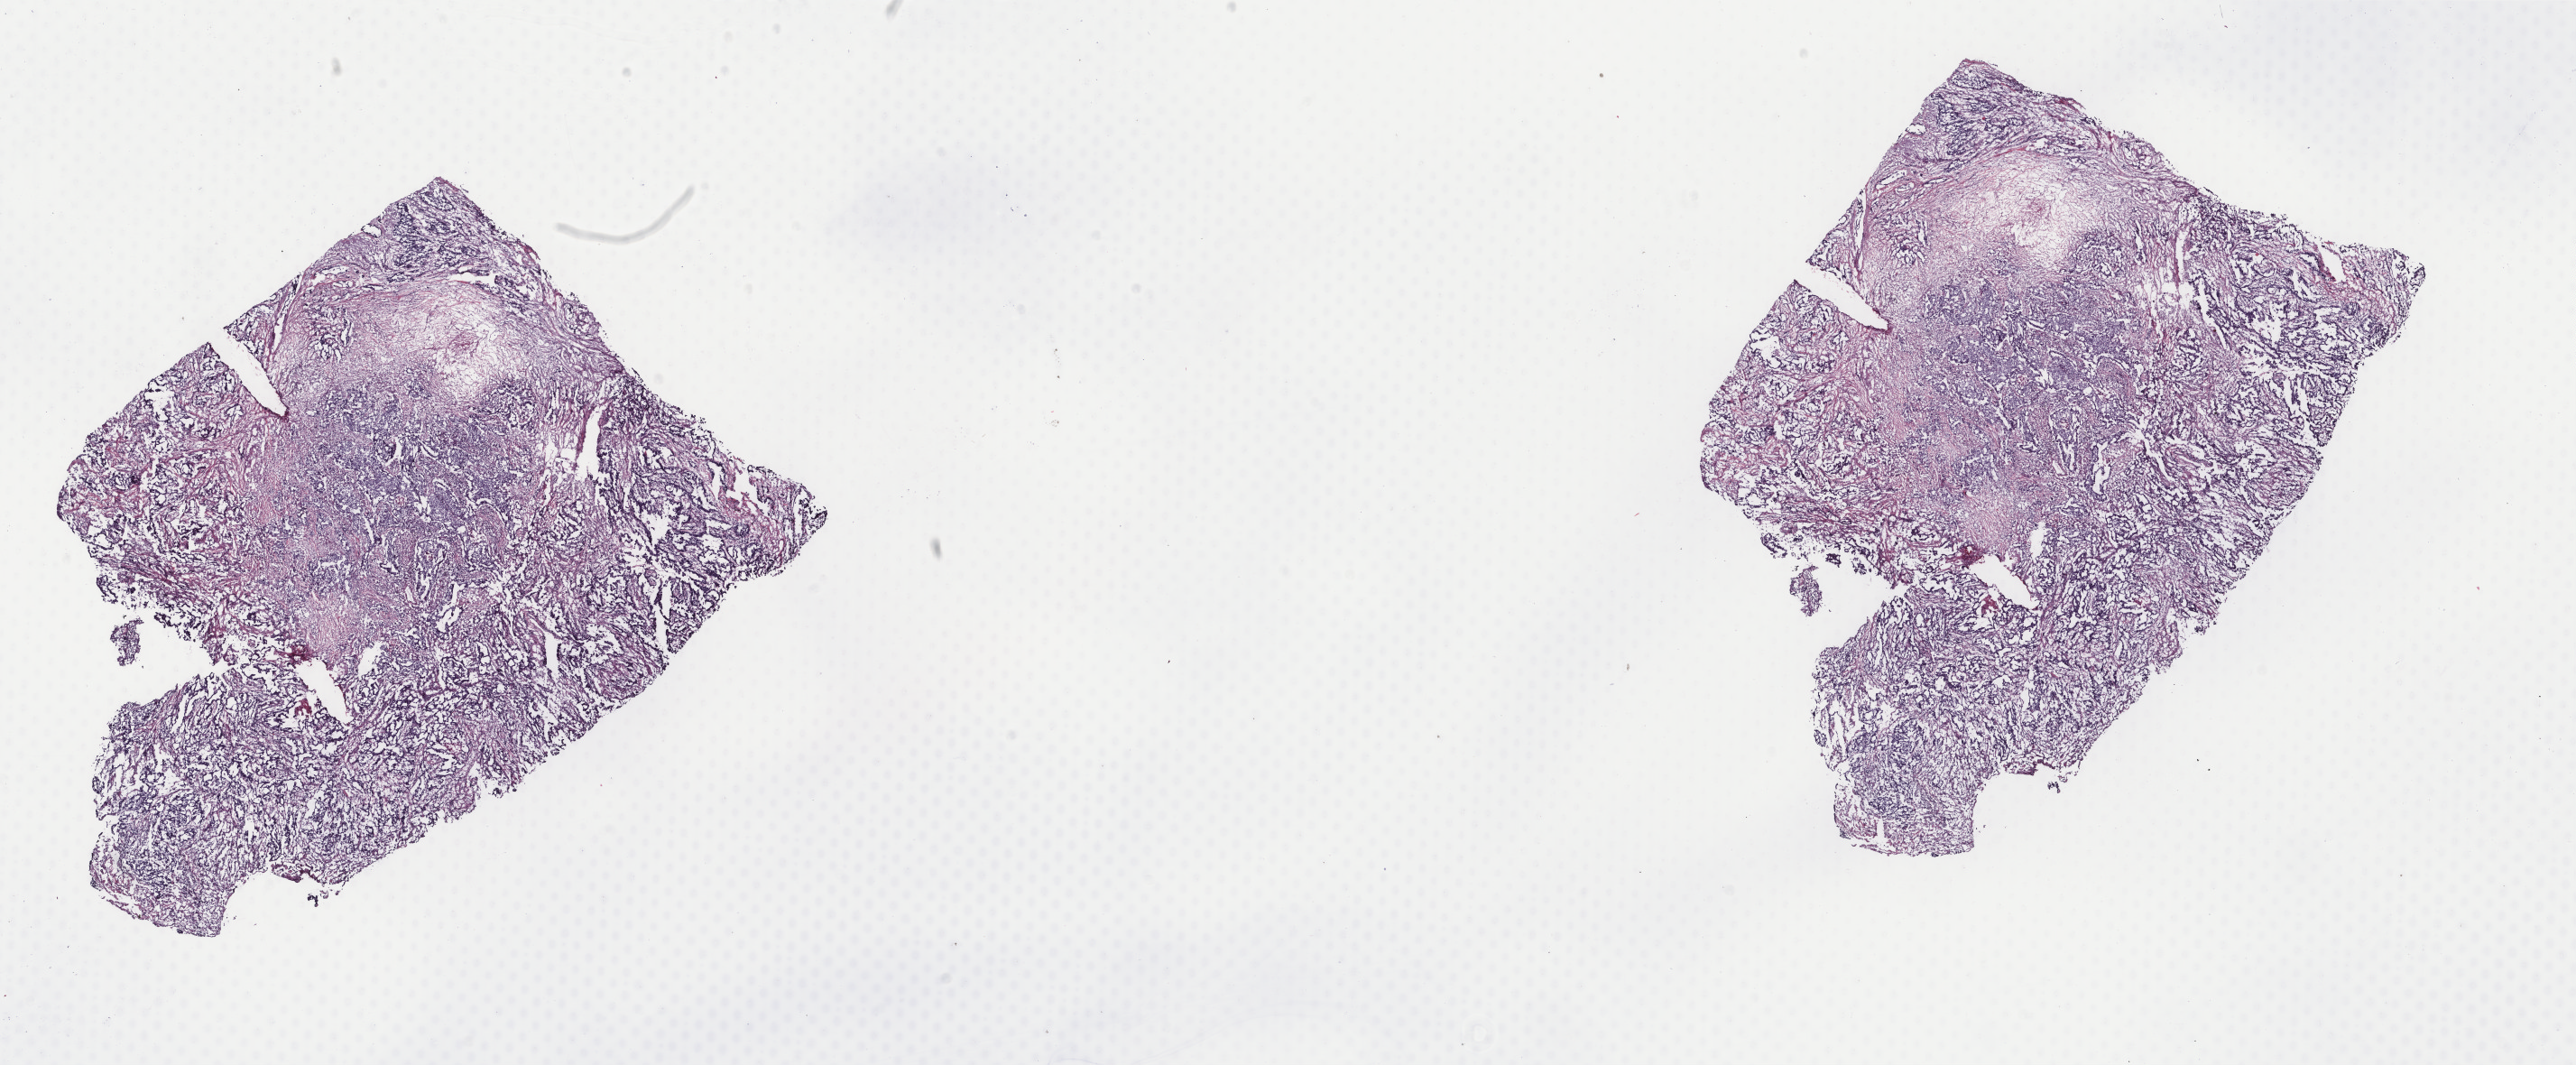
Hematoxylin and eosin (H&E) stained whole-slide image — a low-resolution overview of the entire scanned area, about 22.7 x 9.4 mm; frozen section from the top of the tissue portion; lung, primary tumour sample. Patient: female, age at initial diagnosis 60 years.
Diagnosis: Adenocarcinoma with mixed subtypes (upper lobe, lung).